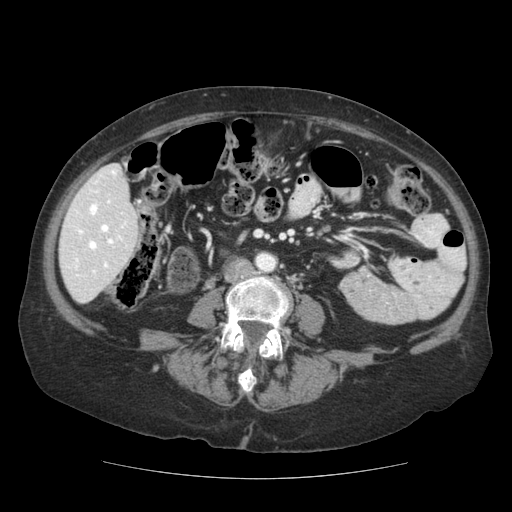
Contrast-enhanced abdominal CT (liver protocol), one axial slice. Position 36 of 111 along the scan axis. Soft-tissue window (W 400 / L 40 HU). 2.5 mm slice thickness. 512 × 512 image matrix, field of view 360 × 360 mm. From the clinical record (not read from this slice): diagnosis: hepatocellular carcinoma (patient treated with transarterial chemoembolisation; whether this scan precedes or follows treatment is not stated here); TNM stage (as recorded): Stage-I; Child-Pugh class: A; tumour differentiation: moderately-poorly differentiated; tumour nodularity: uninodular.
Structures marked on this image (semi-automatically segmented with operator editing):
- liver parenchyma outside the tumour (the mass and vessels are separate outlines, so this box may not span the whole liver): bounding box (x1, y1, x2, y2) in pixels: (58, 164, 138, 302)
- liver vessels: (67, 169, 127, 276)